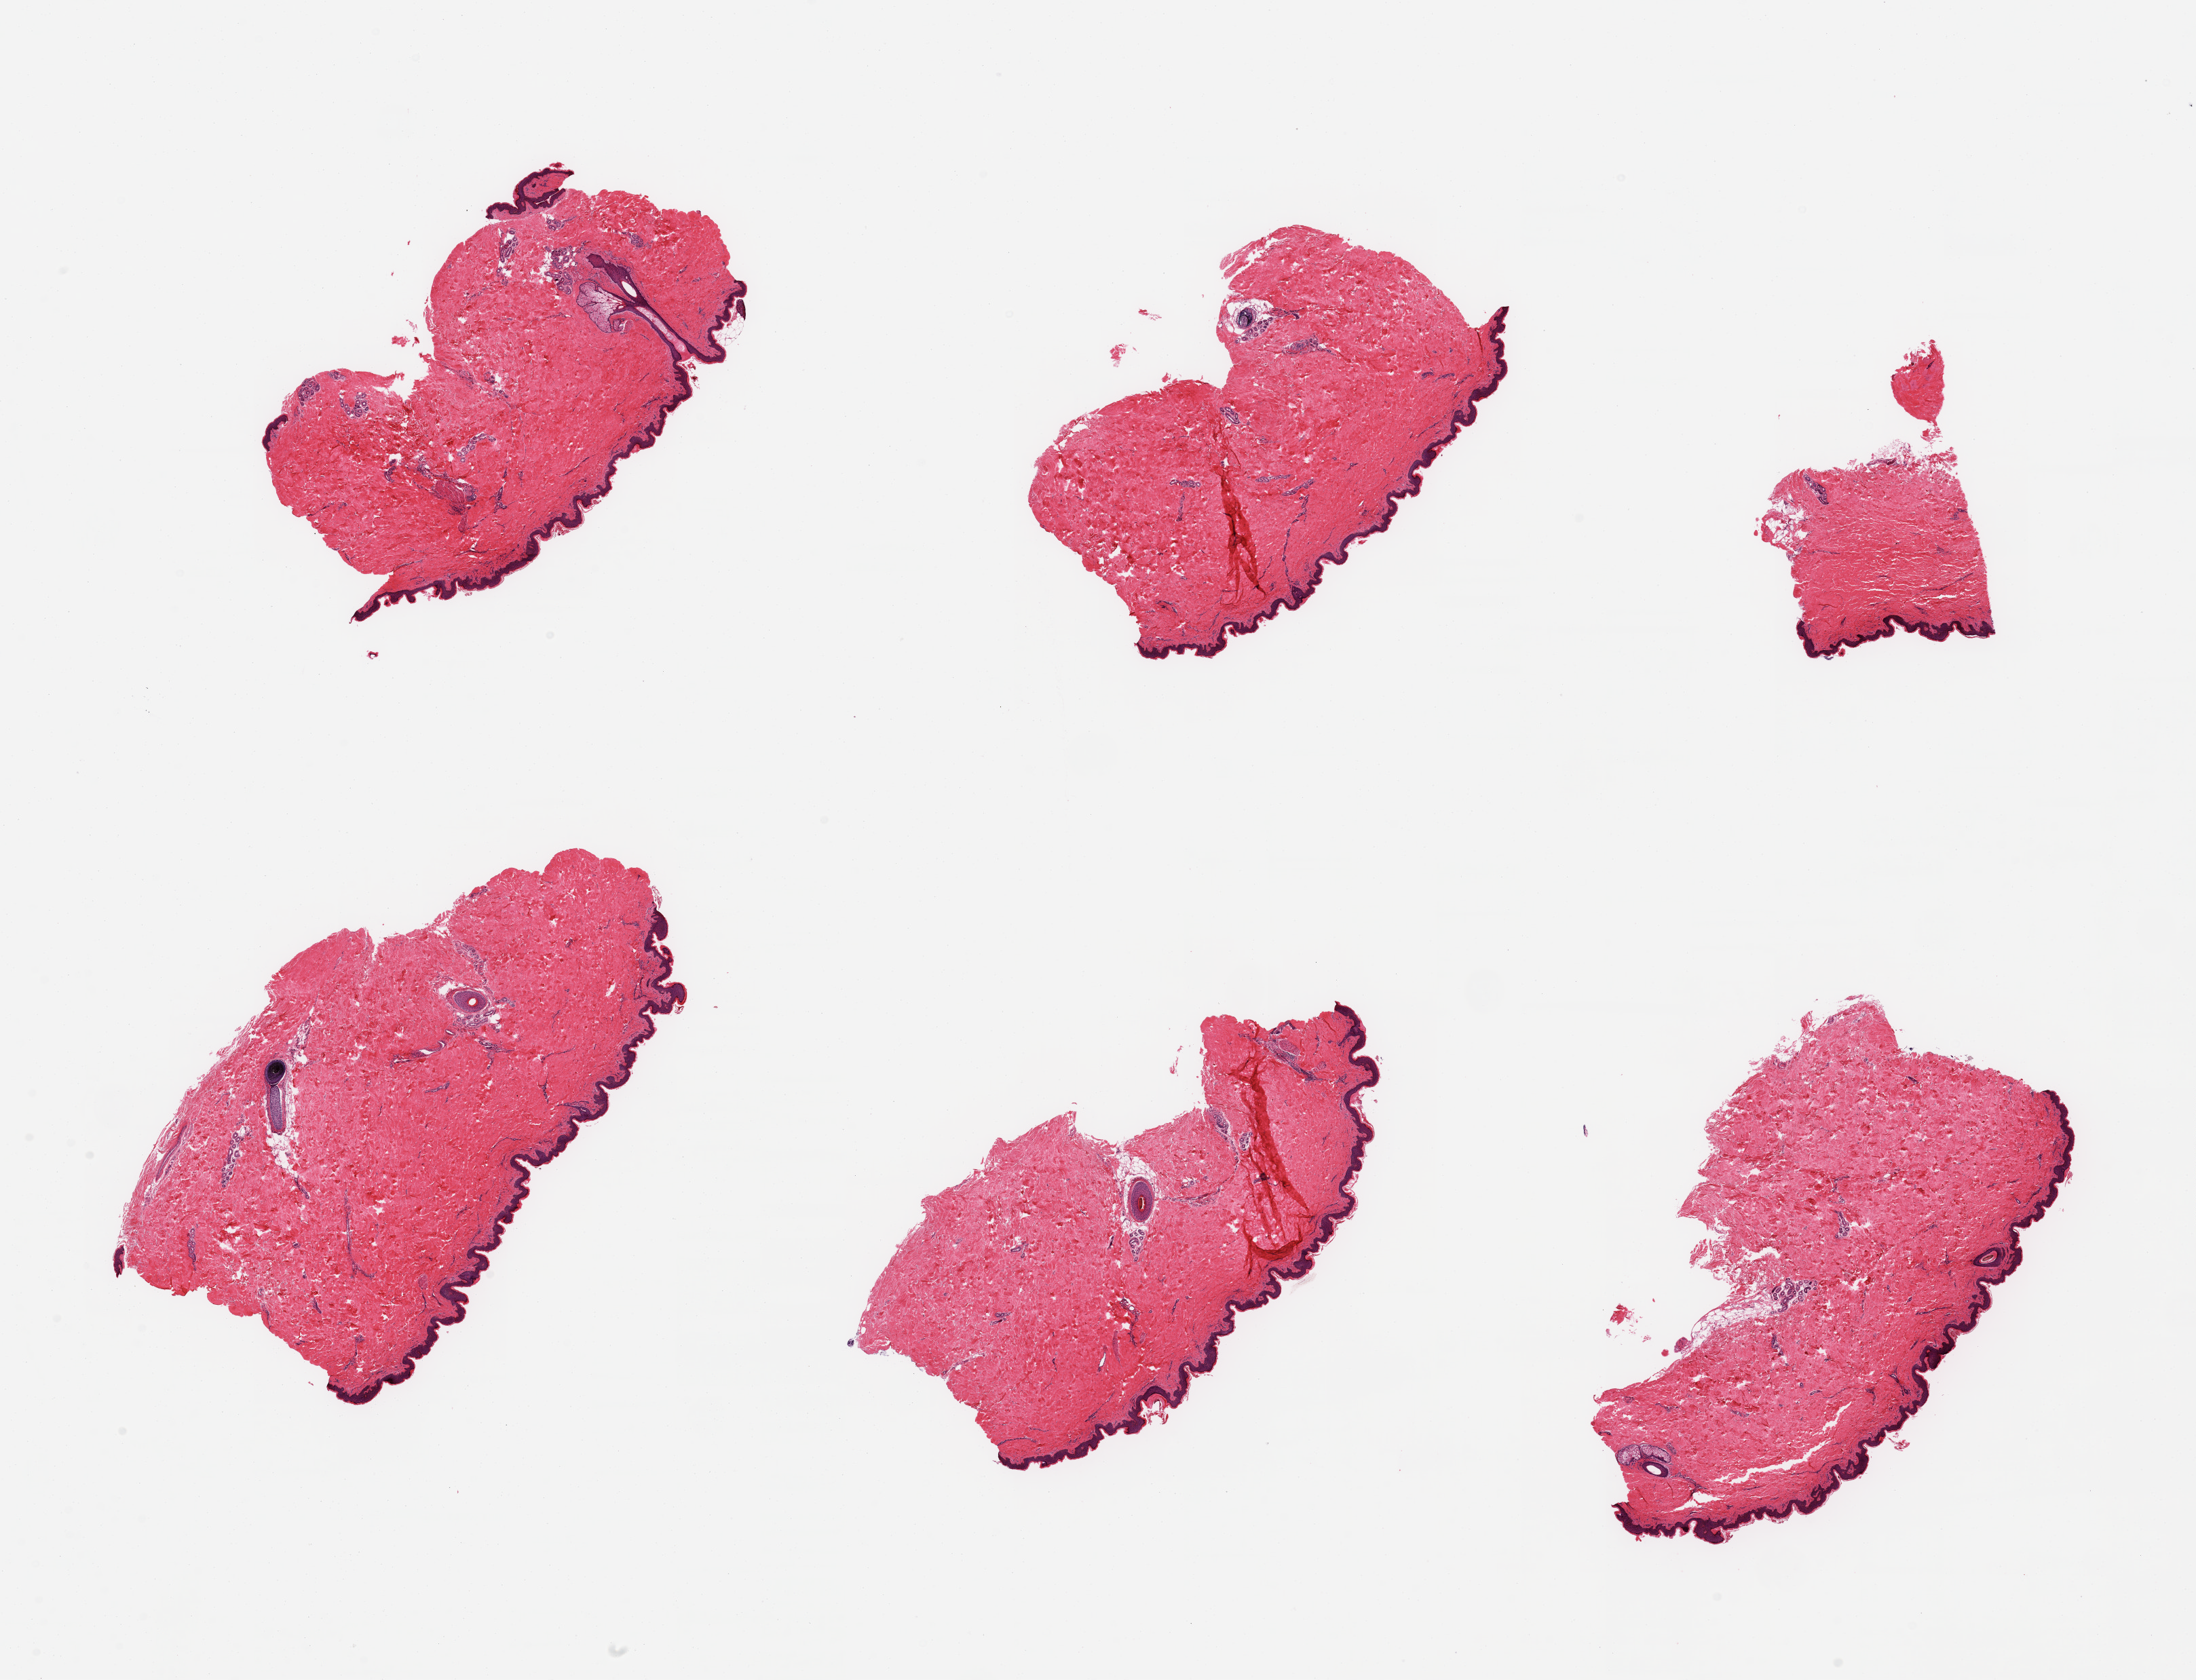
Digitized hematoxylin and eosin (H&E)-stained section, low-resolution overview of the scanned area, about 25.6 x 19.6 mm (acquisition: 20x scan); PAXgene-fixed paraffin-embedded (PFPE) section; target tissue: skin of suprapubic region; tissue donor sample. Donor: male.
Review note (as recorded): 6 pieces; hair bearing skin; small amounts of periadnexal adipose tissue.